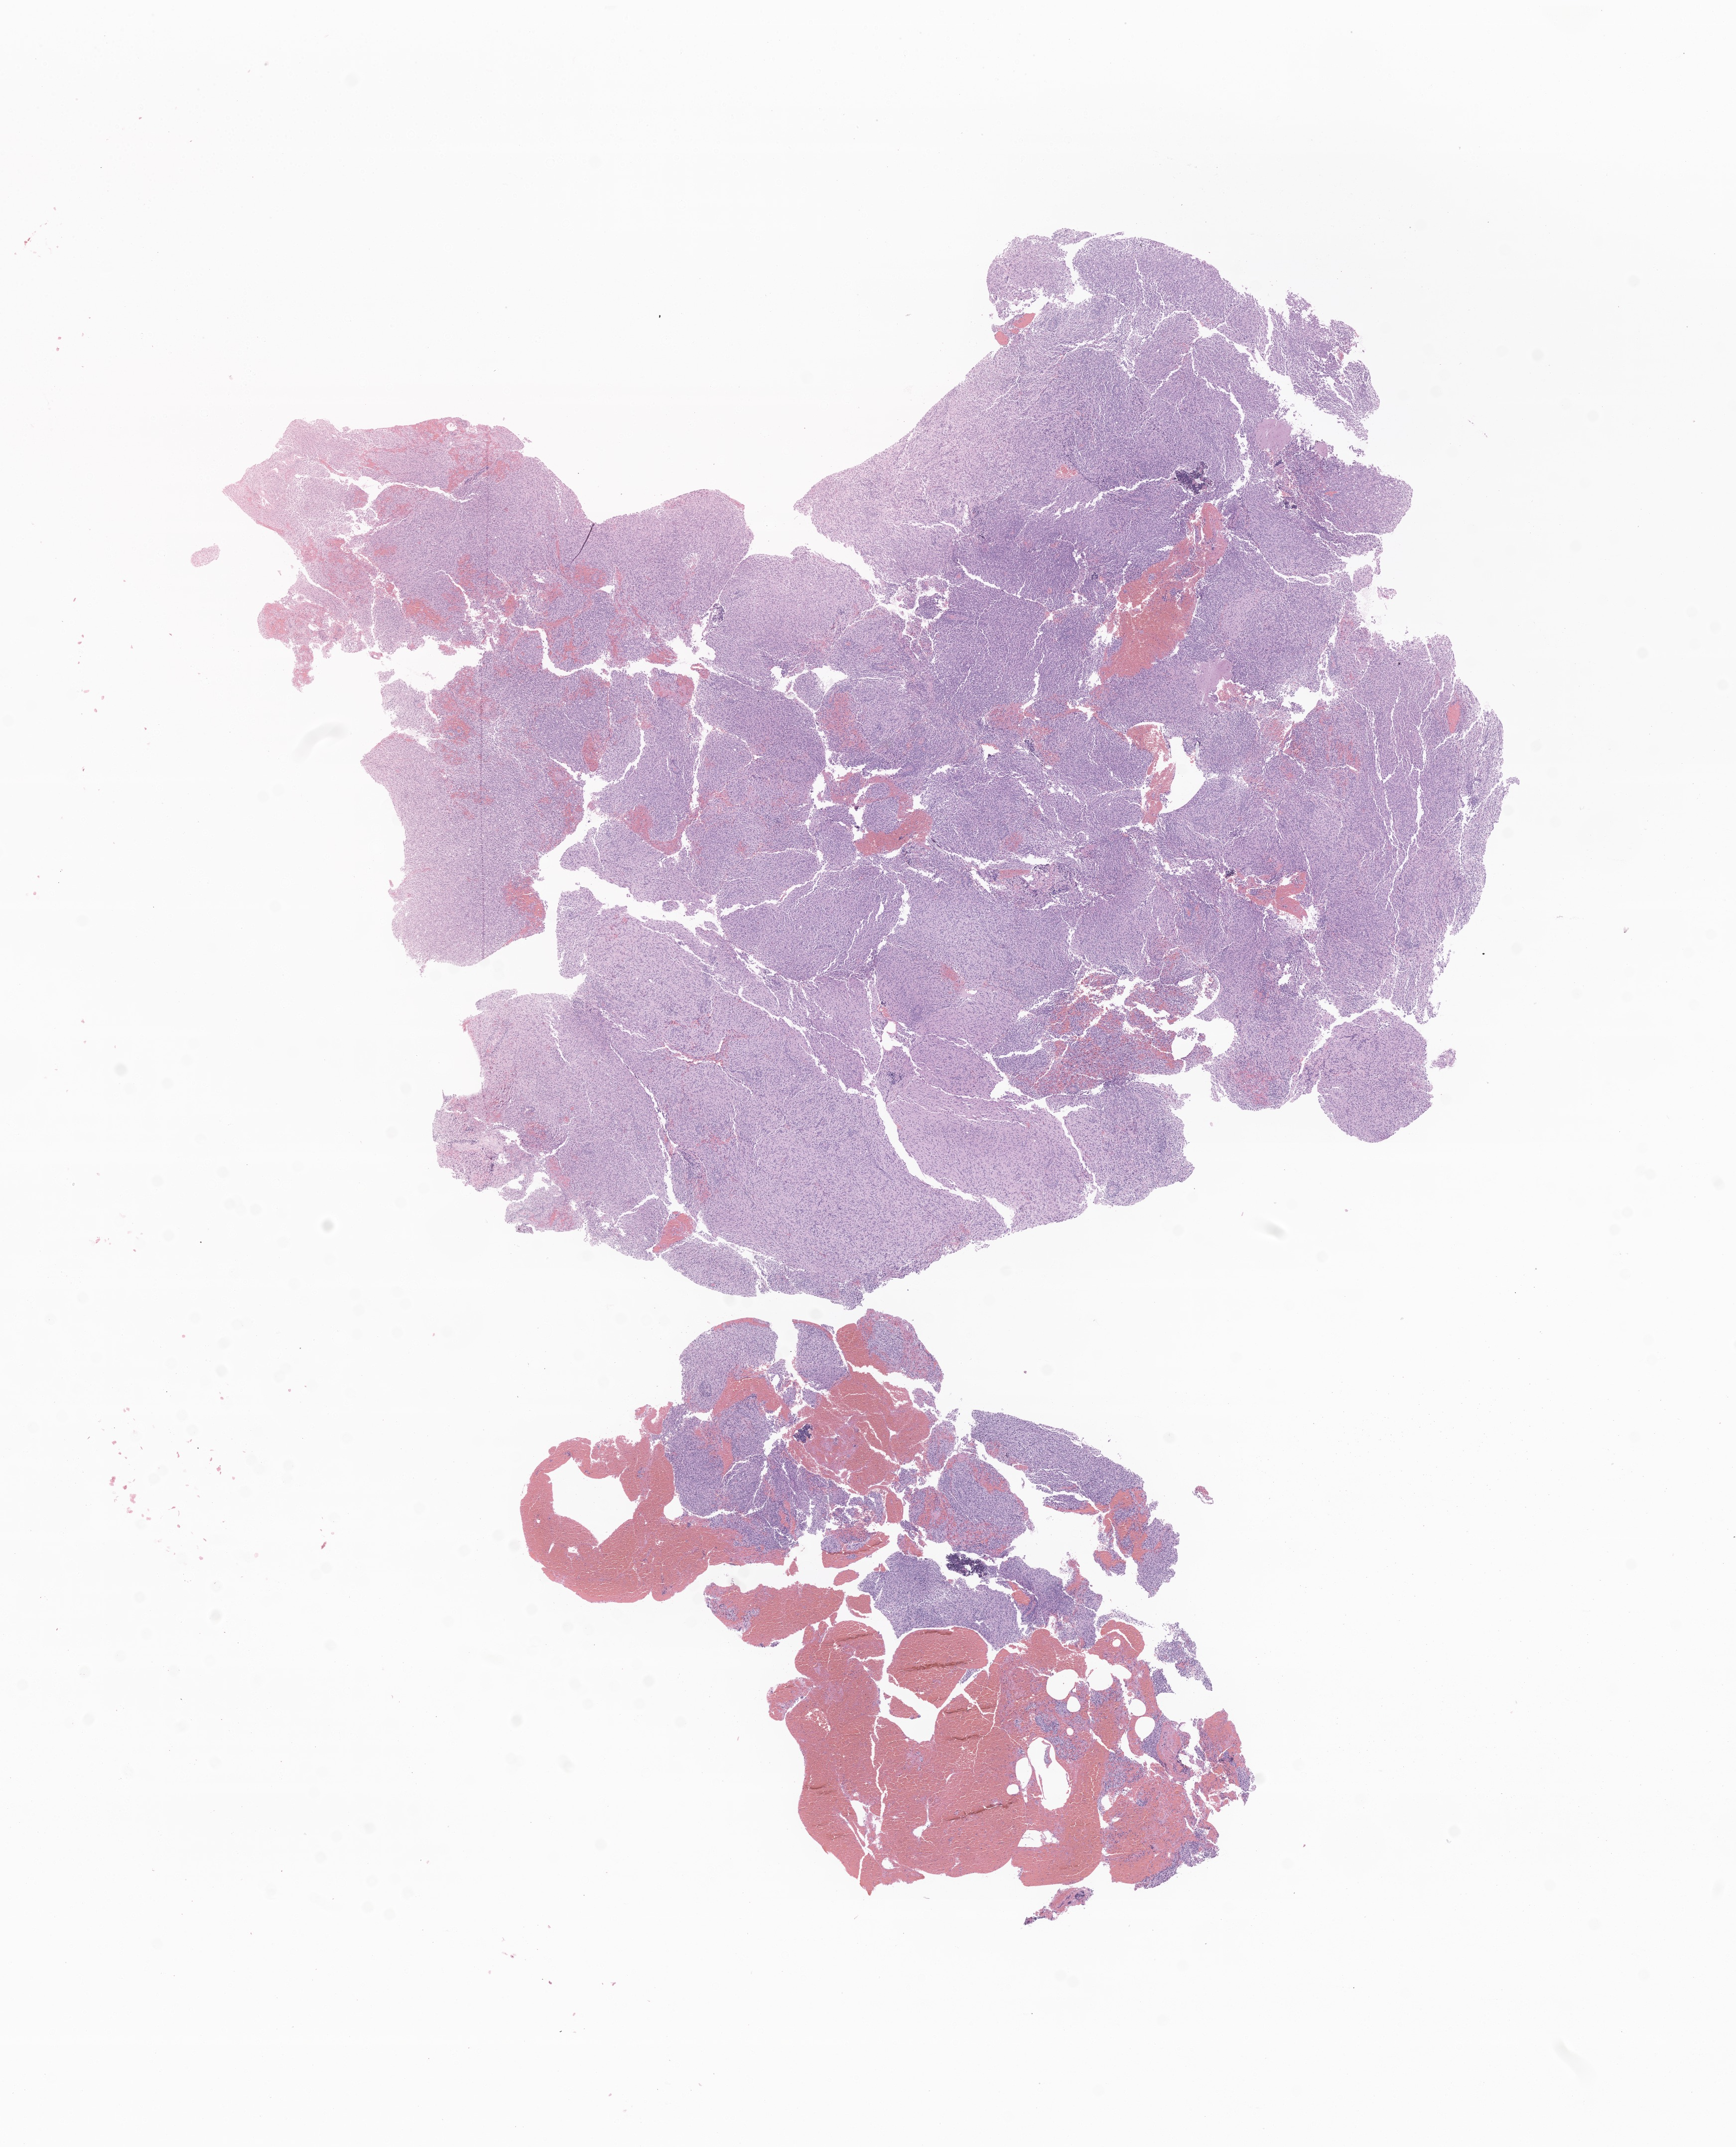
H&E whole-slide image of tumor tissue from the brain — a low-resolution overview of the entire scanned area, about 14.7 x 18.2 mm. FFPE section. Patient: male, age 158 months (13 years 2 months).
Diagnosis (ICD-O-3 morphology term): Glioma, malignant.